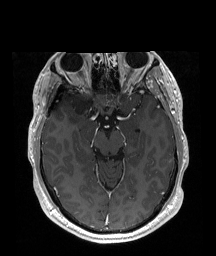
Brain MRI from a brain-tumour surgery series, one axial slice; slice 120 of 192 in the series (ordered by position); T1-weighted post-contrast; 1 mm slice thickness; 216 × 256 image matrix, field of view 219 × 260 mm. Case-level facts recorded for this patient, not image findings: histopathology: Astrocytoma; WHO grade: 2; IDH mutation: yes; tumour location: Right Insular.
Structures marked on this image (expert manual segmentation):
- tumour: bounding box (x1, y1, x2, y2) in pixels: (68, 93, 90, 124)